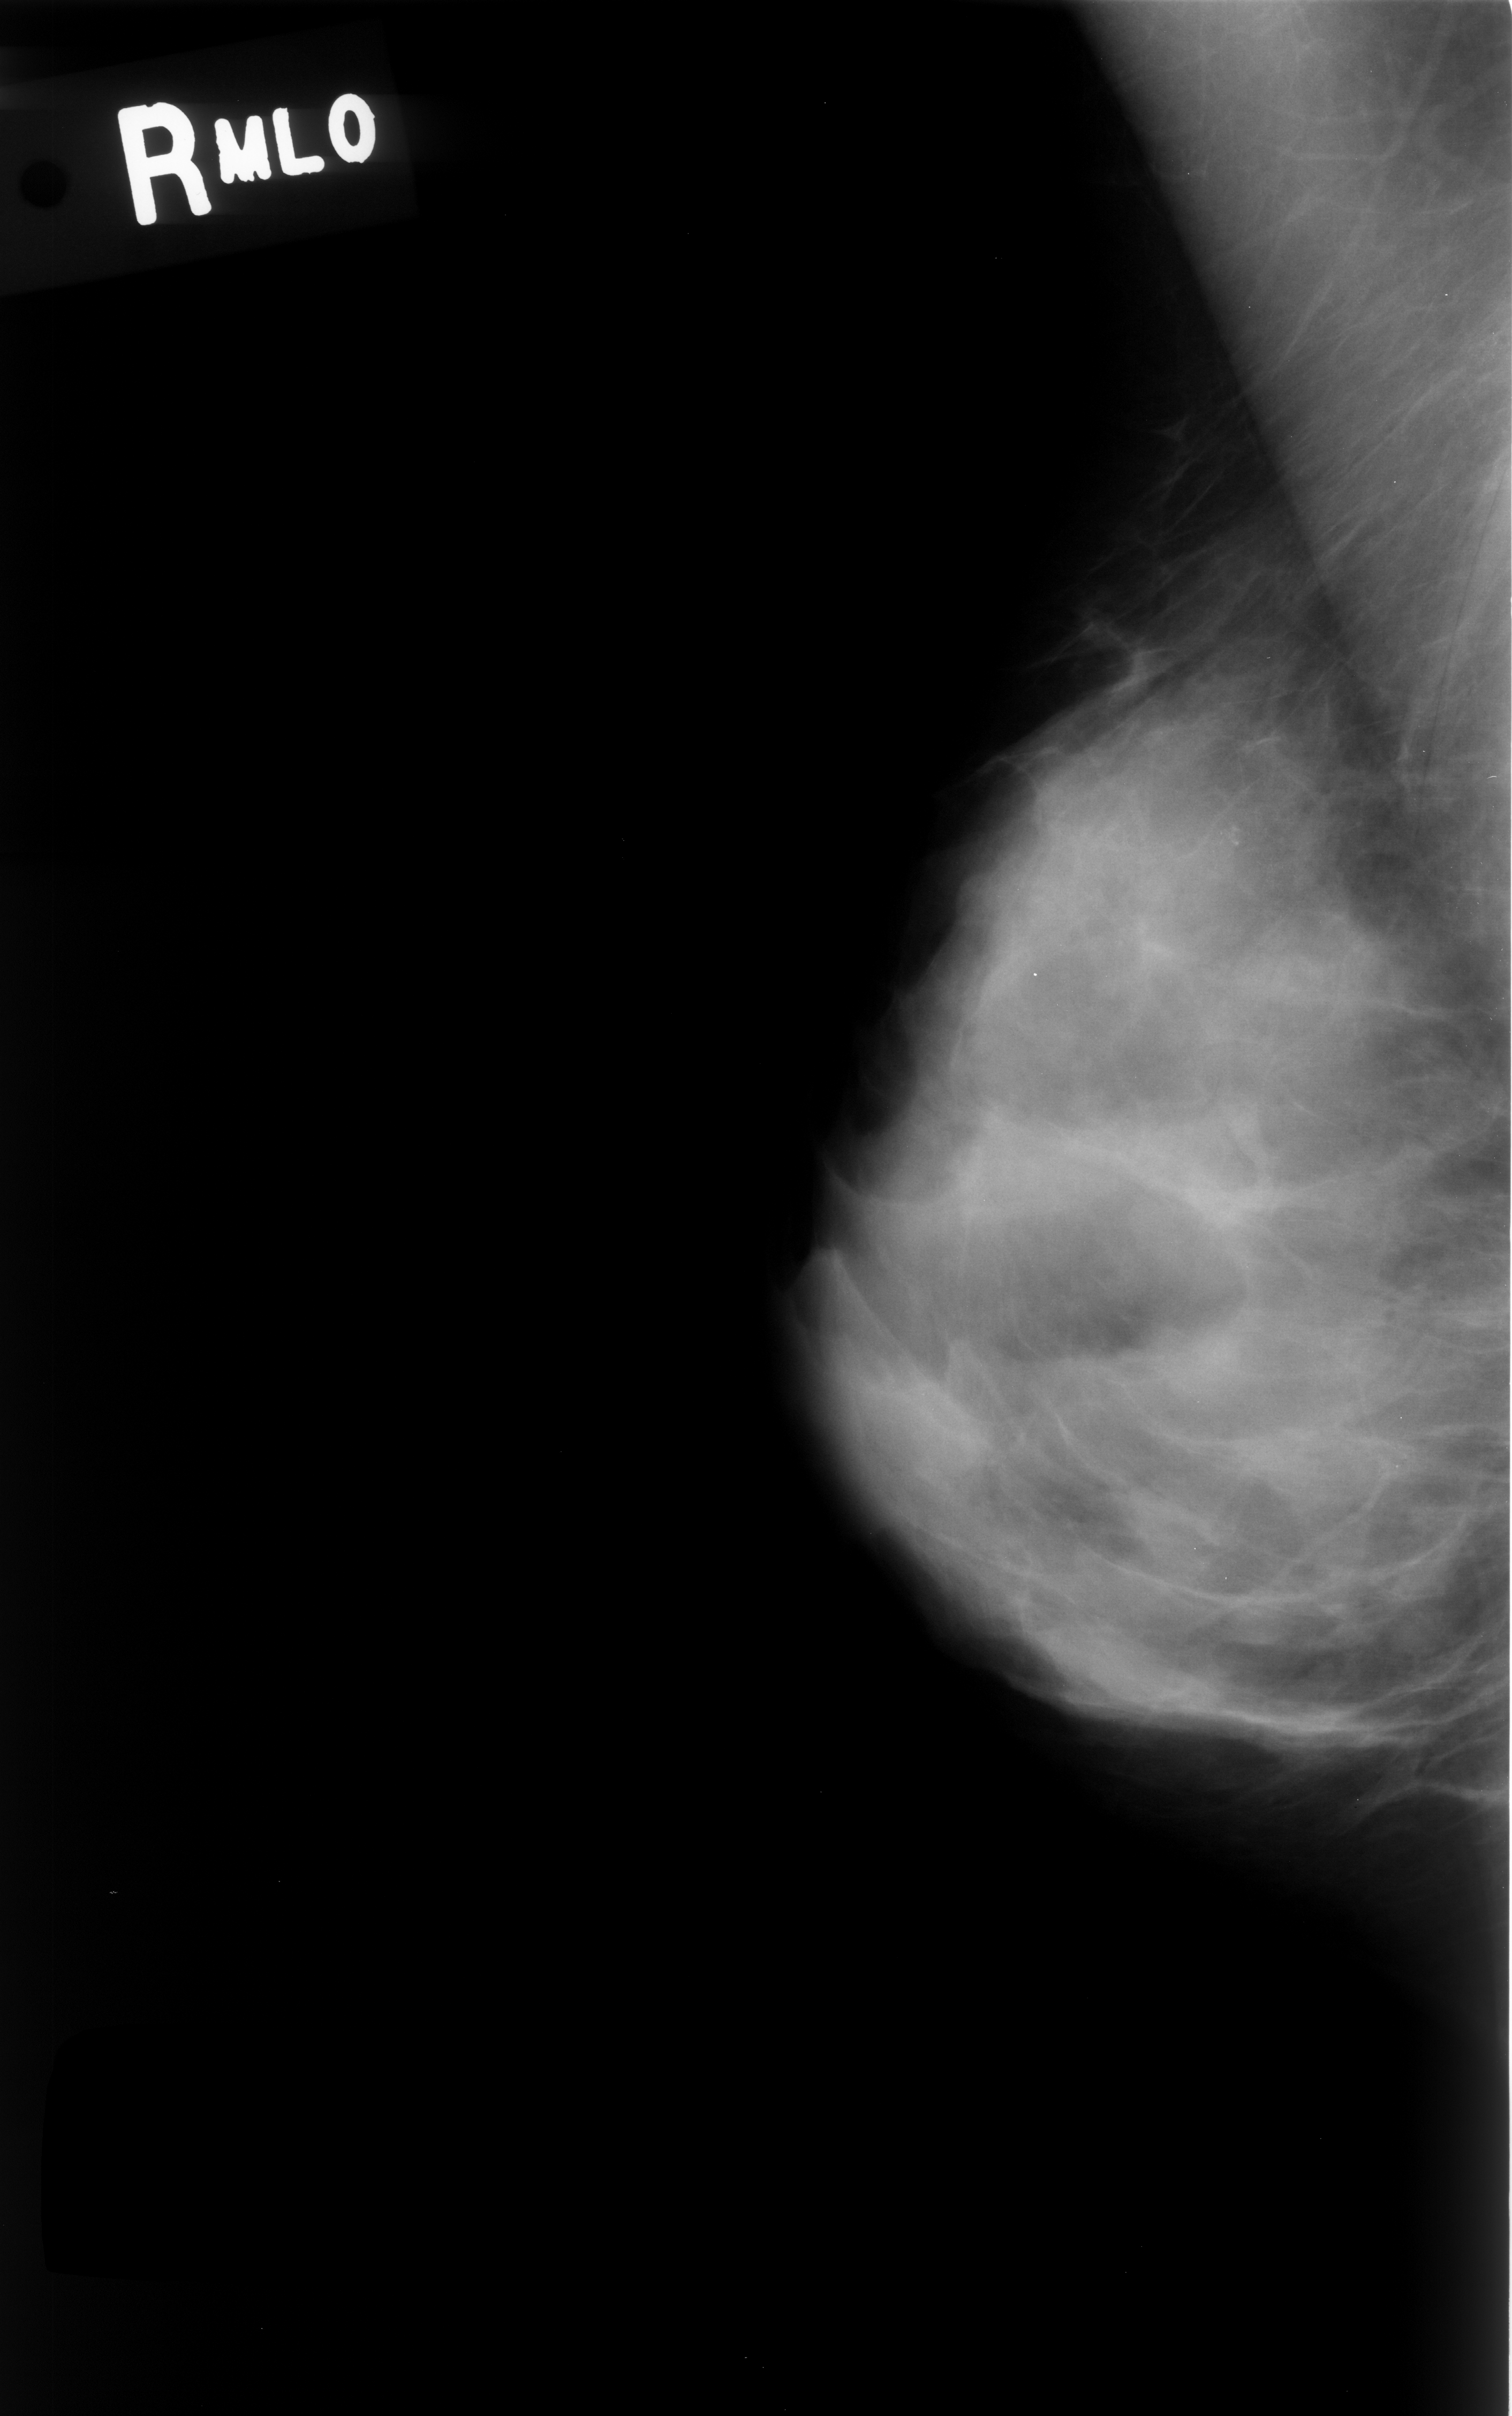
Mammogram (digitized film). Right breast. MLO view. 1512 × 2416 image matrix.
Expert-marked regions of interest on this film, with their recorded descriptors:
- calcifications, morphology amorphous, distribution clustered; BI-RADS assessment category 4; pathology result (as recorded, not read from the image): benign: bounding box <1177,766,1329,943> (left, top, right, bottom; pixels)